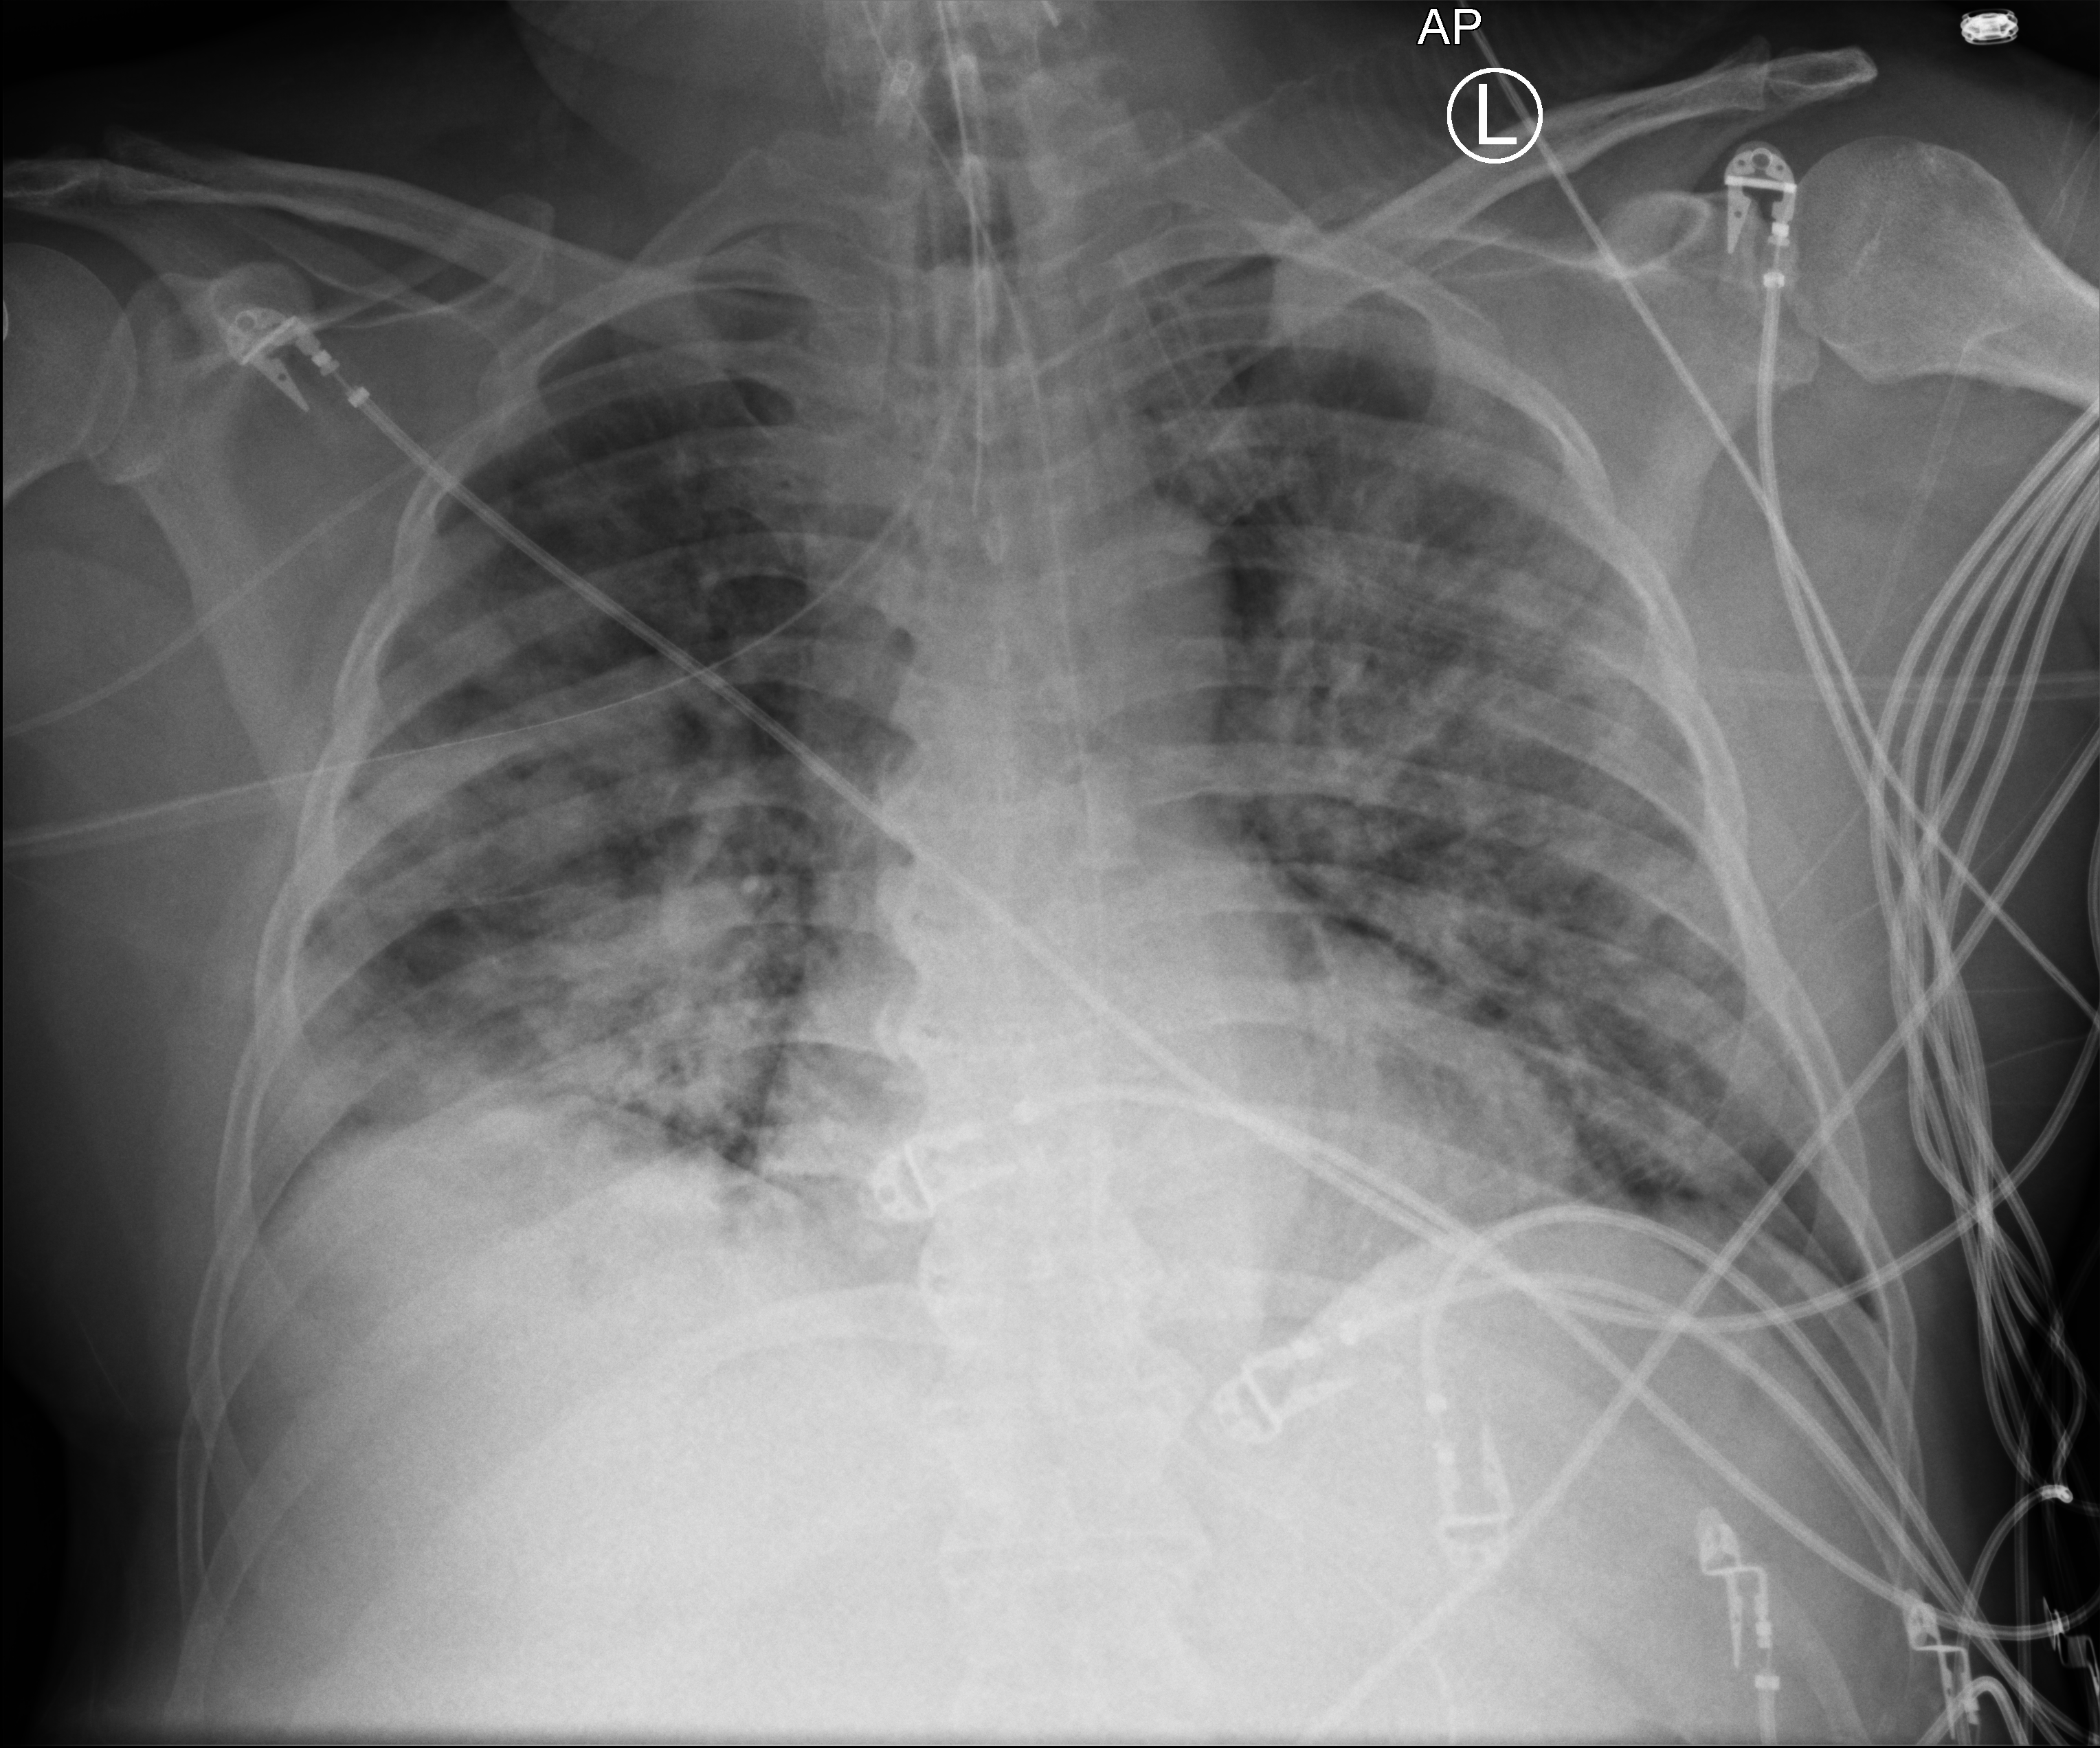
Portable chest radiograph, anteroposterior (AP) projection. Patient hospitalised with COVID-19; male, aged 18–59 years.
Hospital-stay facts (about this admission, not read from this image; timing relative to this image not recorded):
- admitted to intensive care during this hospital stay: yes
- chronic kidney disease (admission record): no